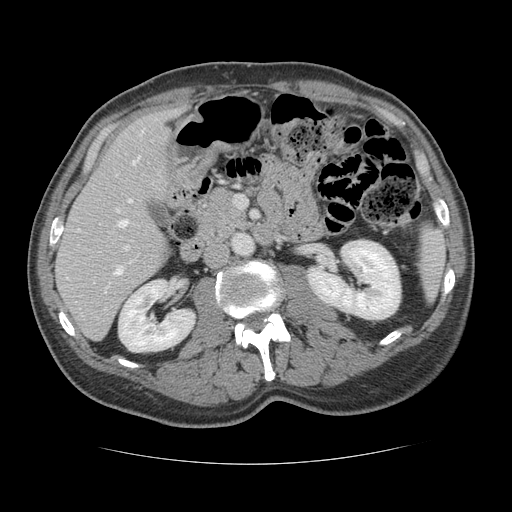
Contrast-enhanced abdominal CT, one axial slice. Slice 60 of 134 in the series (ordered by position). Reconstruction kernel STANDARD. 120 kVp. Intravenous contrast given. Soft-tissue window (W 400 / L 40 HU). 512 × 512 image matrix, field of view 377 × 377 mm. Male patient, age 68 years. From the clinical record (not read from this slice): diagnosis: colorectal cancer liver metastases, imaged before liver resection; multiple liver metastases: yes; largest metastasis: 2.2 cm; disease in both lobes: no.
Annotated regions visible in this slice (expert manual segmentation):
- hepatic veins: box from (x=116, y=131) to (x=143, y=227) px
- liver: (x=57, y=111)–(x=174, y=339)
- planned liver remnant (the part of the liver to remain after resection): (x=57, y=111)–(x=175, y=335)
- portal vein (with intrahepatic branches): (x=115, y=209)–(x=131, y=275)